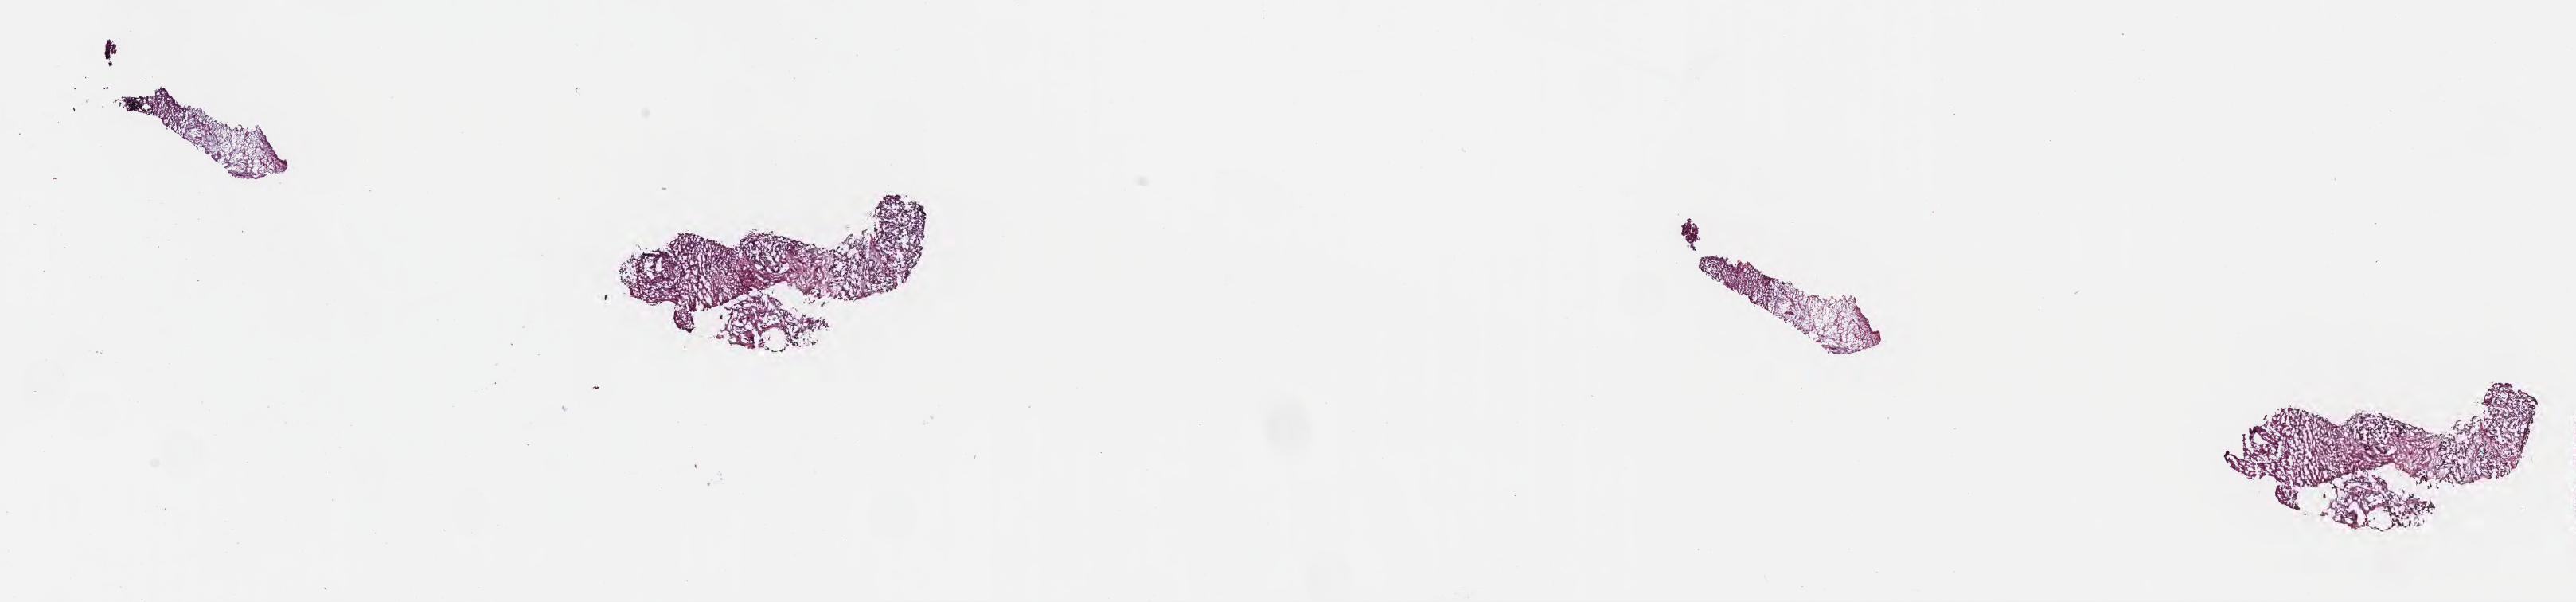
Whole-slide image, hematoxylin and eosin (H&E) stain, a low-resolution overview of the entire scanned area, about 26.2 x 6.1 mm, frozen section (tissue freezing medium), specimen: metastatic tumor tissue, resected from liver. Male patient; age at initial diagnosis 51 years. Slide review estimates, as recorded: tumor cells 100%, tumor nuclei 60%, stromal cells 0%, necrosis 0%, normal cells 0%. Inflammatory infiltration, as recorded: lymphocyte infiltration 0%, monocyte infiltration 0%, neutrophil infiltration 0%.
Patient diagnosis (primary): Adenocarcinoma, NOS.